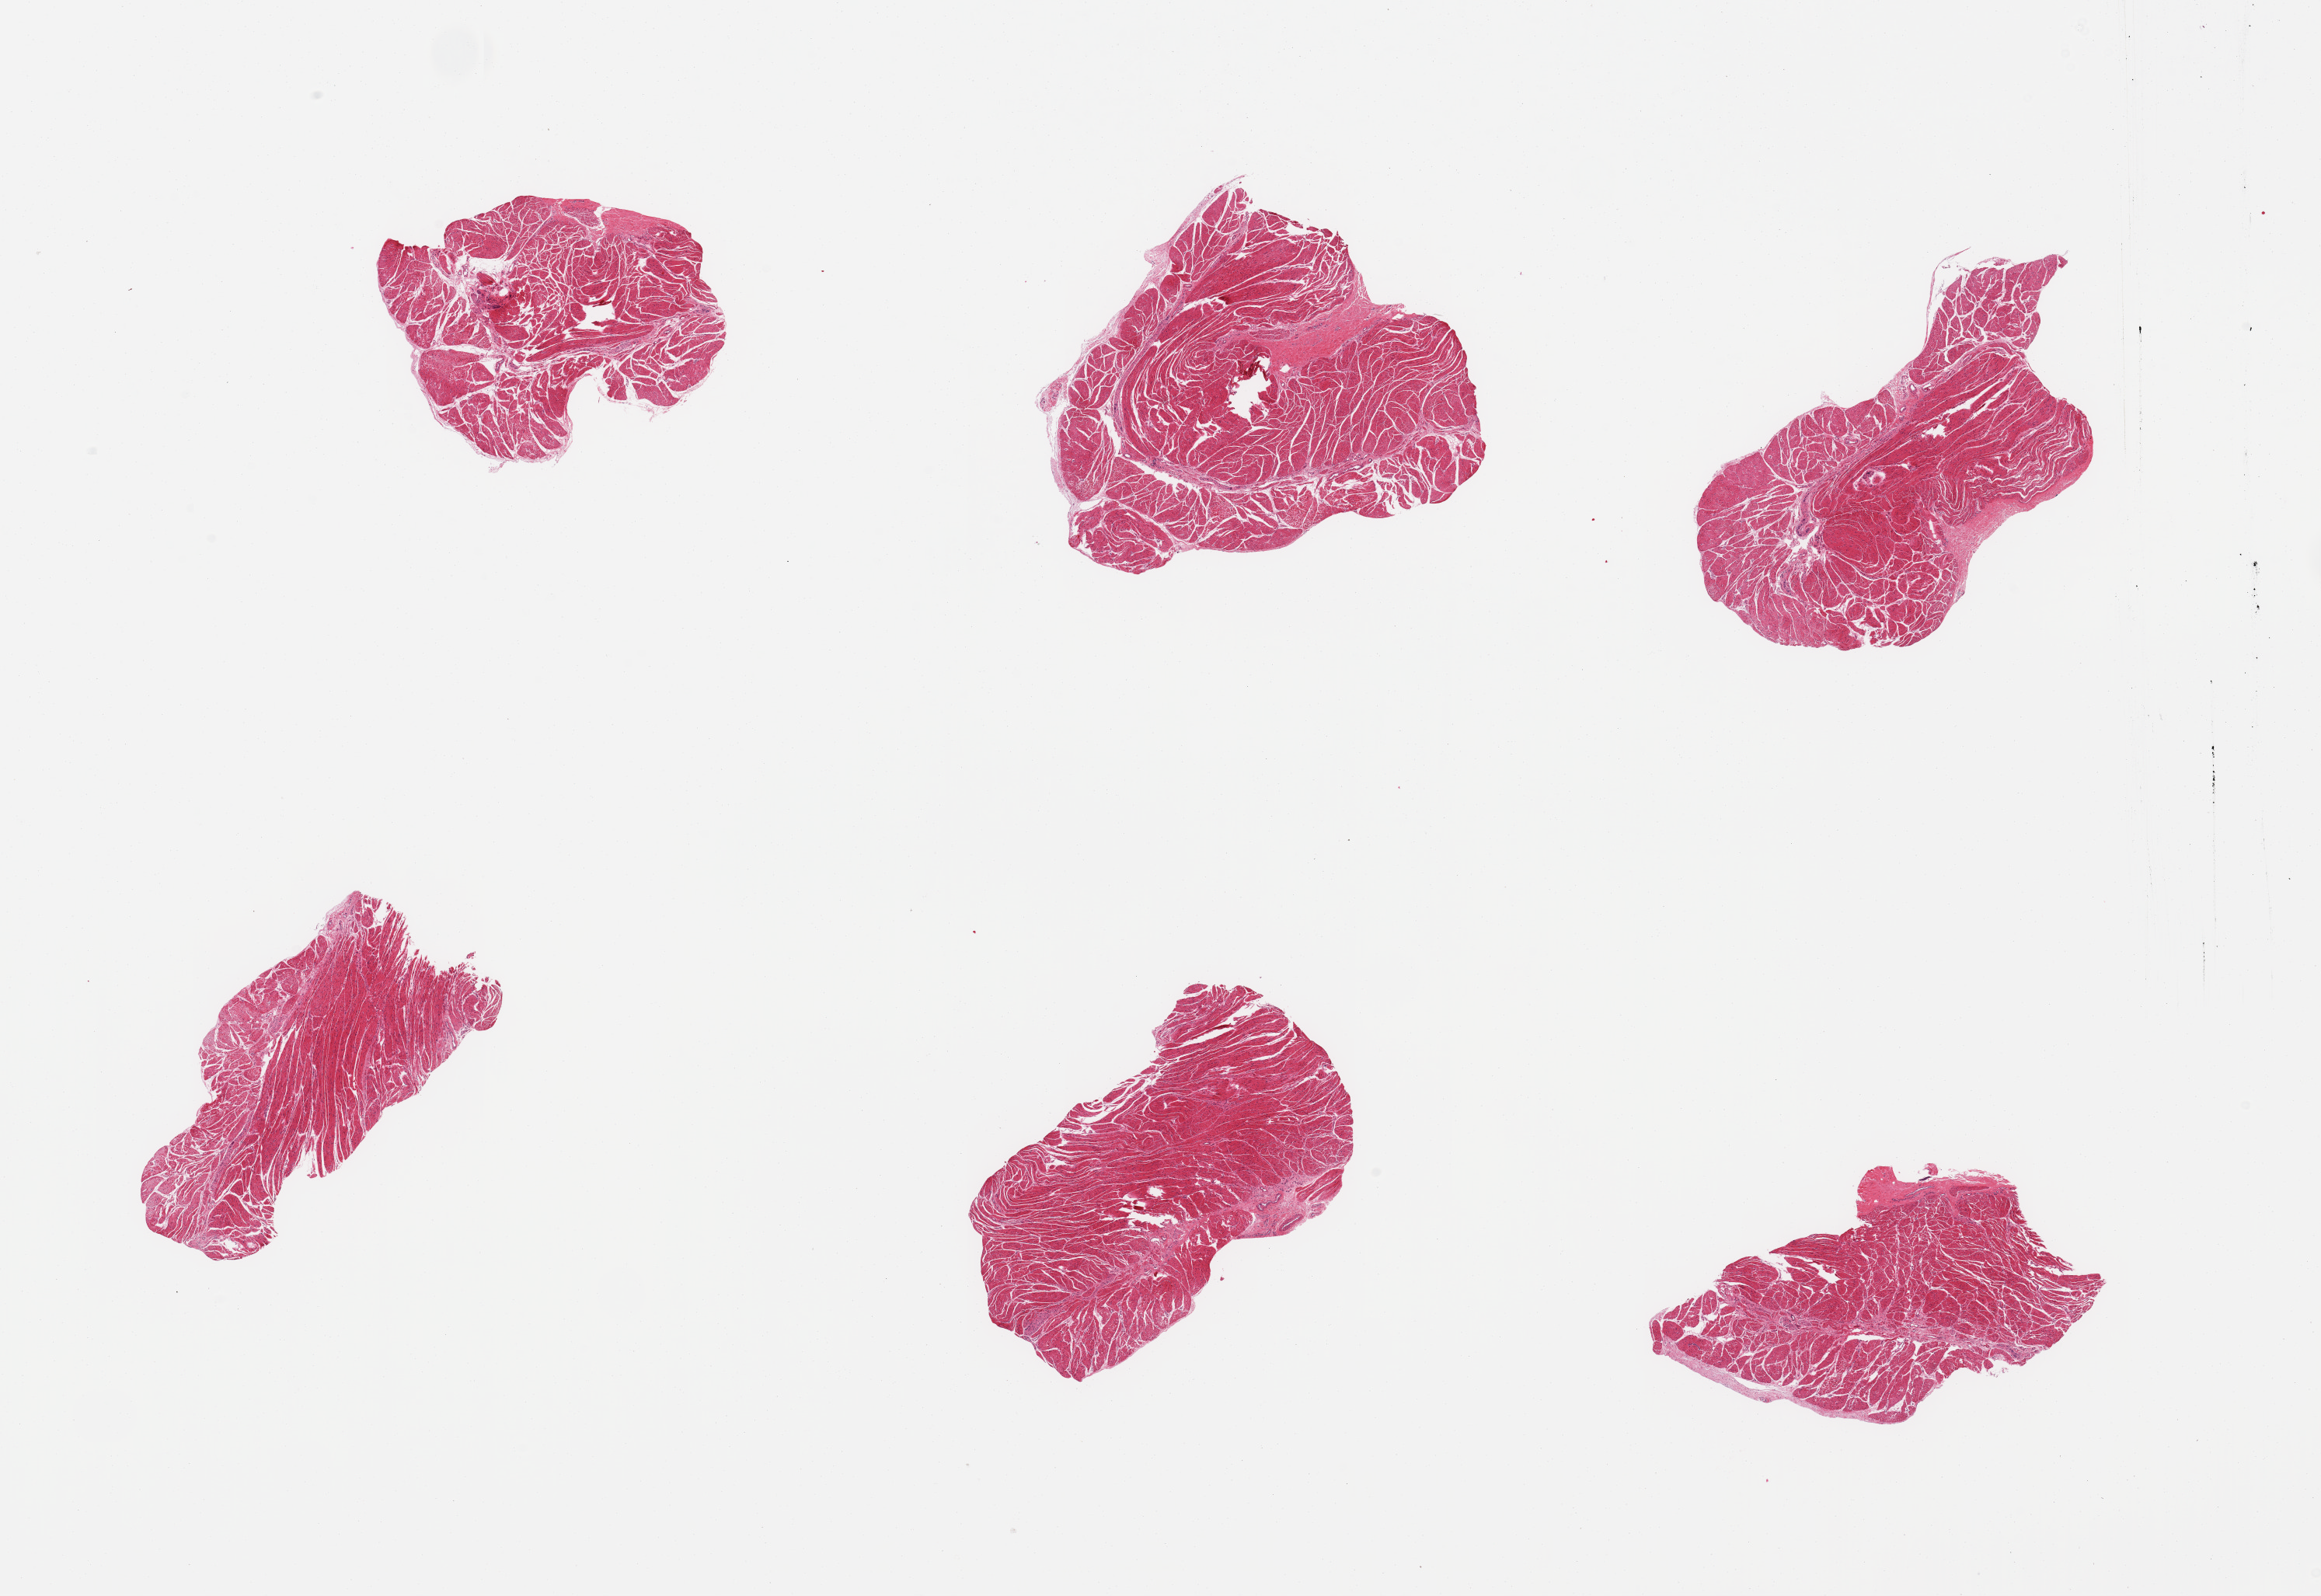
Whole-slide image, H&E stain — low-resolution overview of the scanned area, about 23.6 x 16.2 mm (slide scanned at 20x). PAXgene-fixed paraffin-embedded (PFPE) section. Target tissue: gastroesophageal junction. Donor tissue sample. Donor: female.
Pathologist's review note for this sample: 6 pieces; target muscularis.